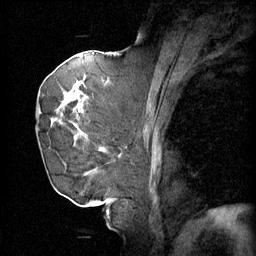
Breast MRI (dynamic contrast-enhanced), one sagittal slice; slice 29 of 60 in the series (ordered by position); 4 images stored at this slice position (order not interpretable as contrast timing); 1.5 T; TE 4.2 ms, TR 11 ms; 256 × 256 image matrix. Patient: female, 72 years.
Annotated regions visible in this slice (semi-automatic segmentation, software-assisted and operator-edited):
- analysis volume of interest (the breast-tissue region the enhancement analysis was run in; not a lesion): box from (x=43, y=68) to (x=109, y=163) px
- tumour enhancement mask (voxels above the 70 % enhancement threshold inside the analysis volume of interest): (x=43, y=78)–(x=106, y=151)